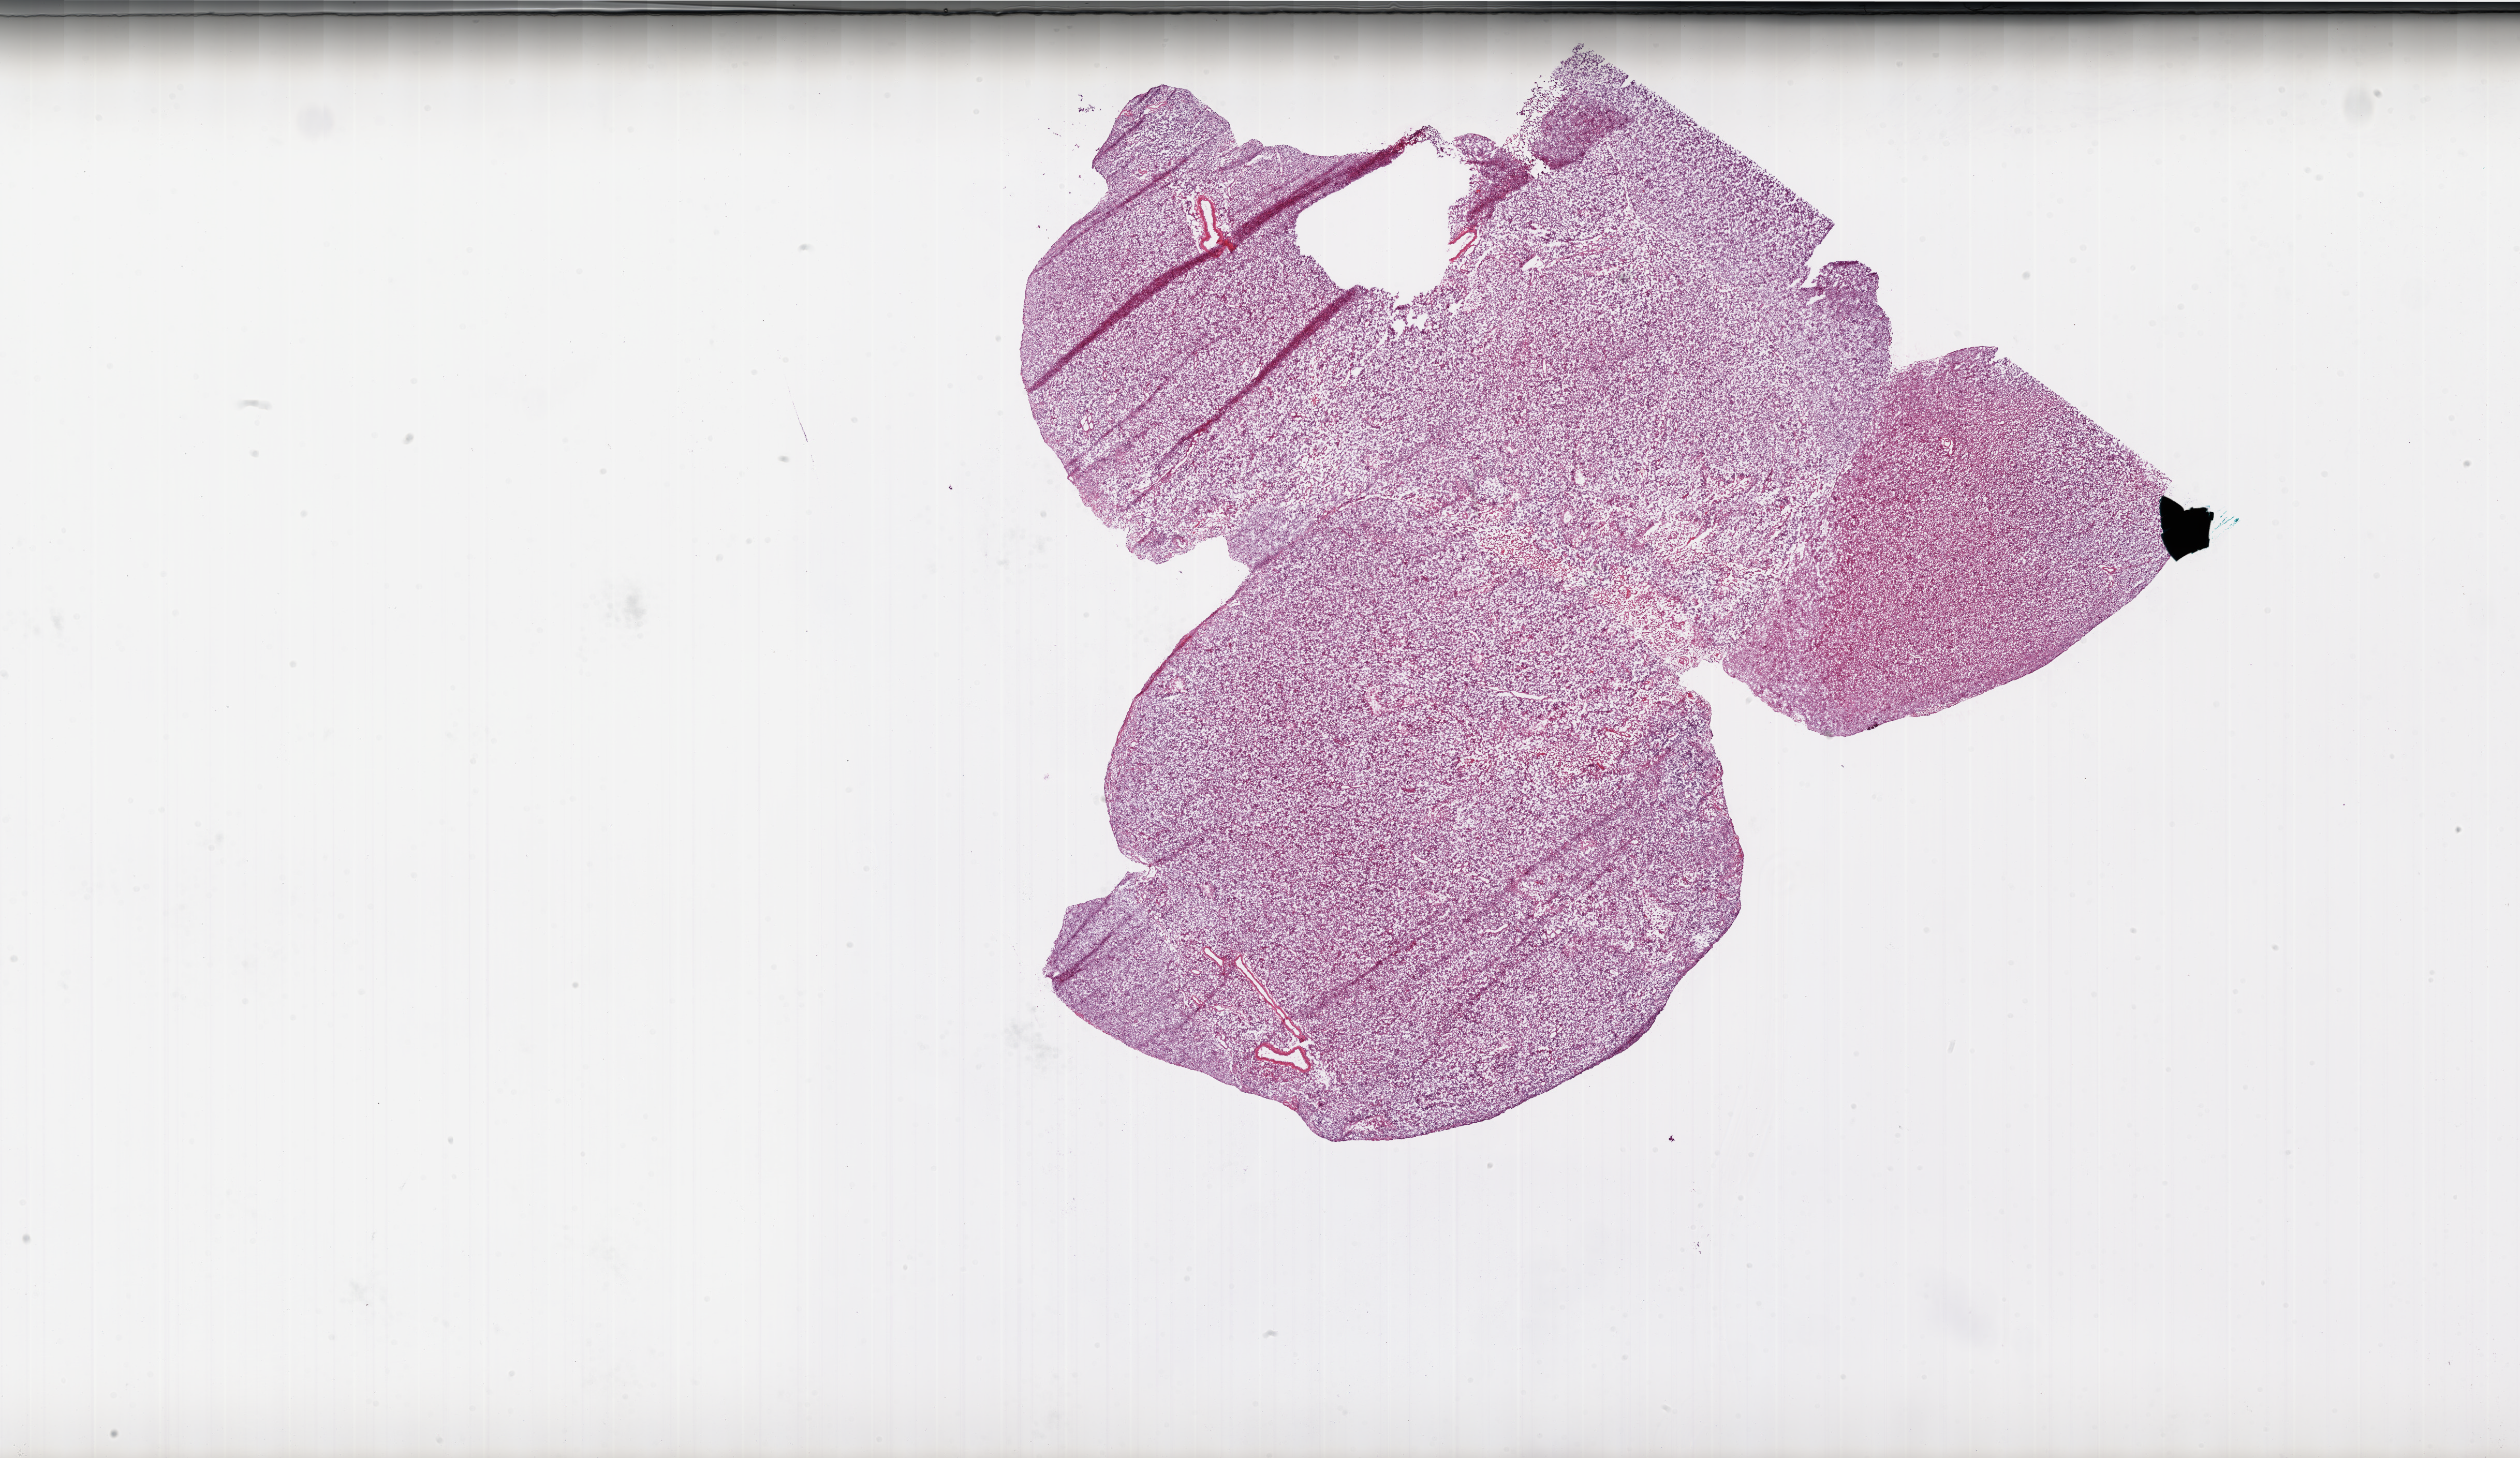
H&E whole-slide image — shown as a low-resolution overview of the whole scanned area (about 39.0 x 22.5 mm, acquisition: 20x scan). Frozen section from the bottom of the tissue portion. Sample: primary tumour, brain. Female, age 78 years at initial diagnosis. Slide review estimates, as recorded: tumour cells 100%, tumour nuclei 100%, normal cells 0%, stromal cells 0%, necrosis 0%. Infiltration values recorded for this section: lymphocyte infiltration 0%, monocyte infiltration 0%, neutrophil infiltration 0%.
Histologic diagnosis: Glioblastoma.